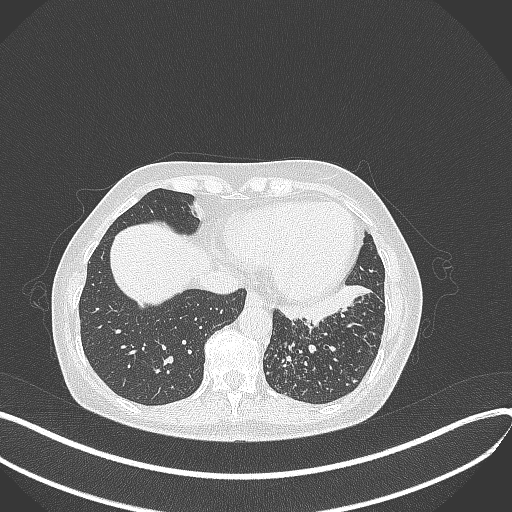
Chest CT, one axial slice. Position 111 of 429 along the scan axis. Lung window (W 1500 / L -600 HU). 1 mm slice thickness. 512 × 512 image matrix, field of view 400 × 400 mm. Patient: female, 63 years. From the clinical record (not read from this slice): clinical TNM (as recorded): T1b N0 M0; histopathological grade: G2-3.
Structures marked on this image (bounding box drawn by a radiologist):
- lung tumour (recorded histology: adenocarcinoma): bounding box <279,285,375,324> (left, top, right, bottom; pixels)